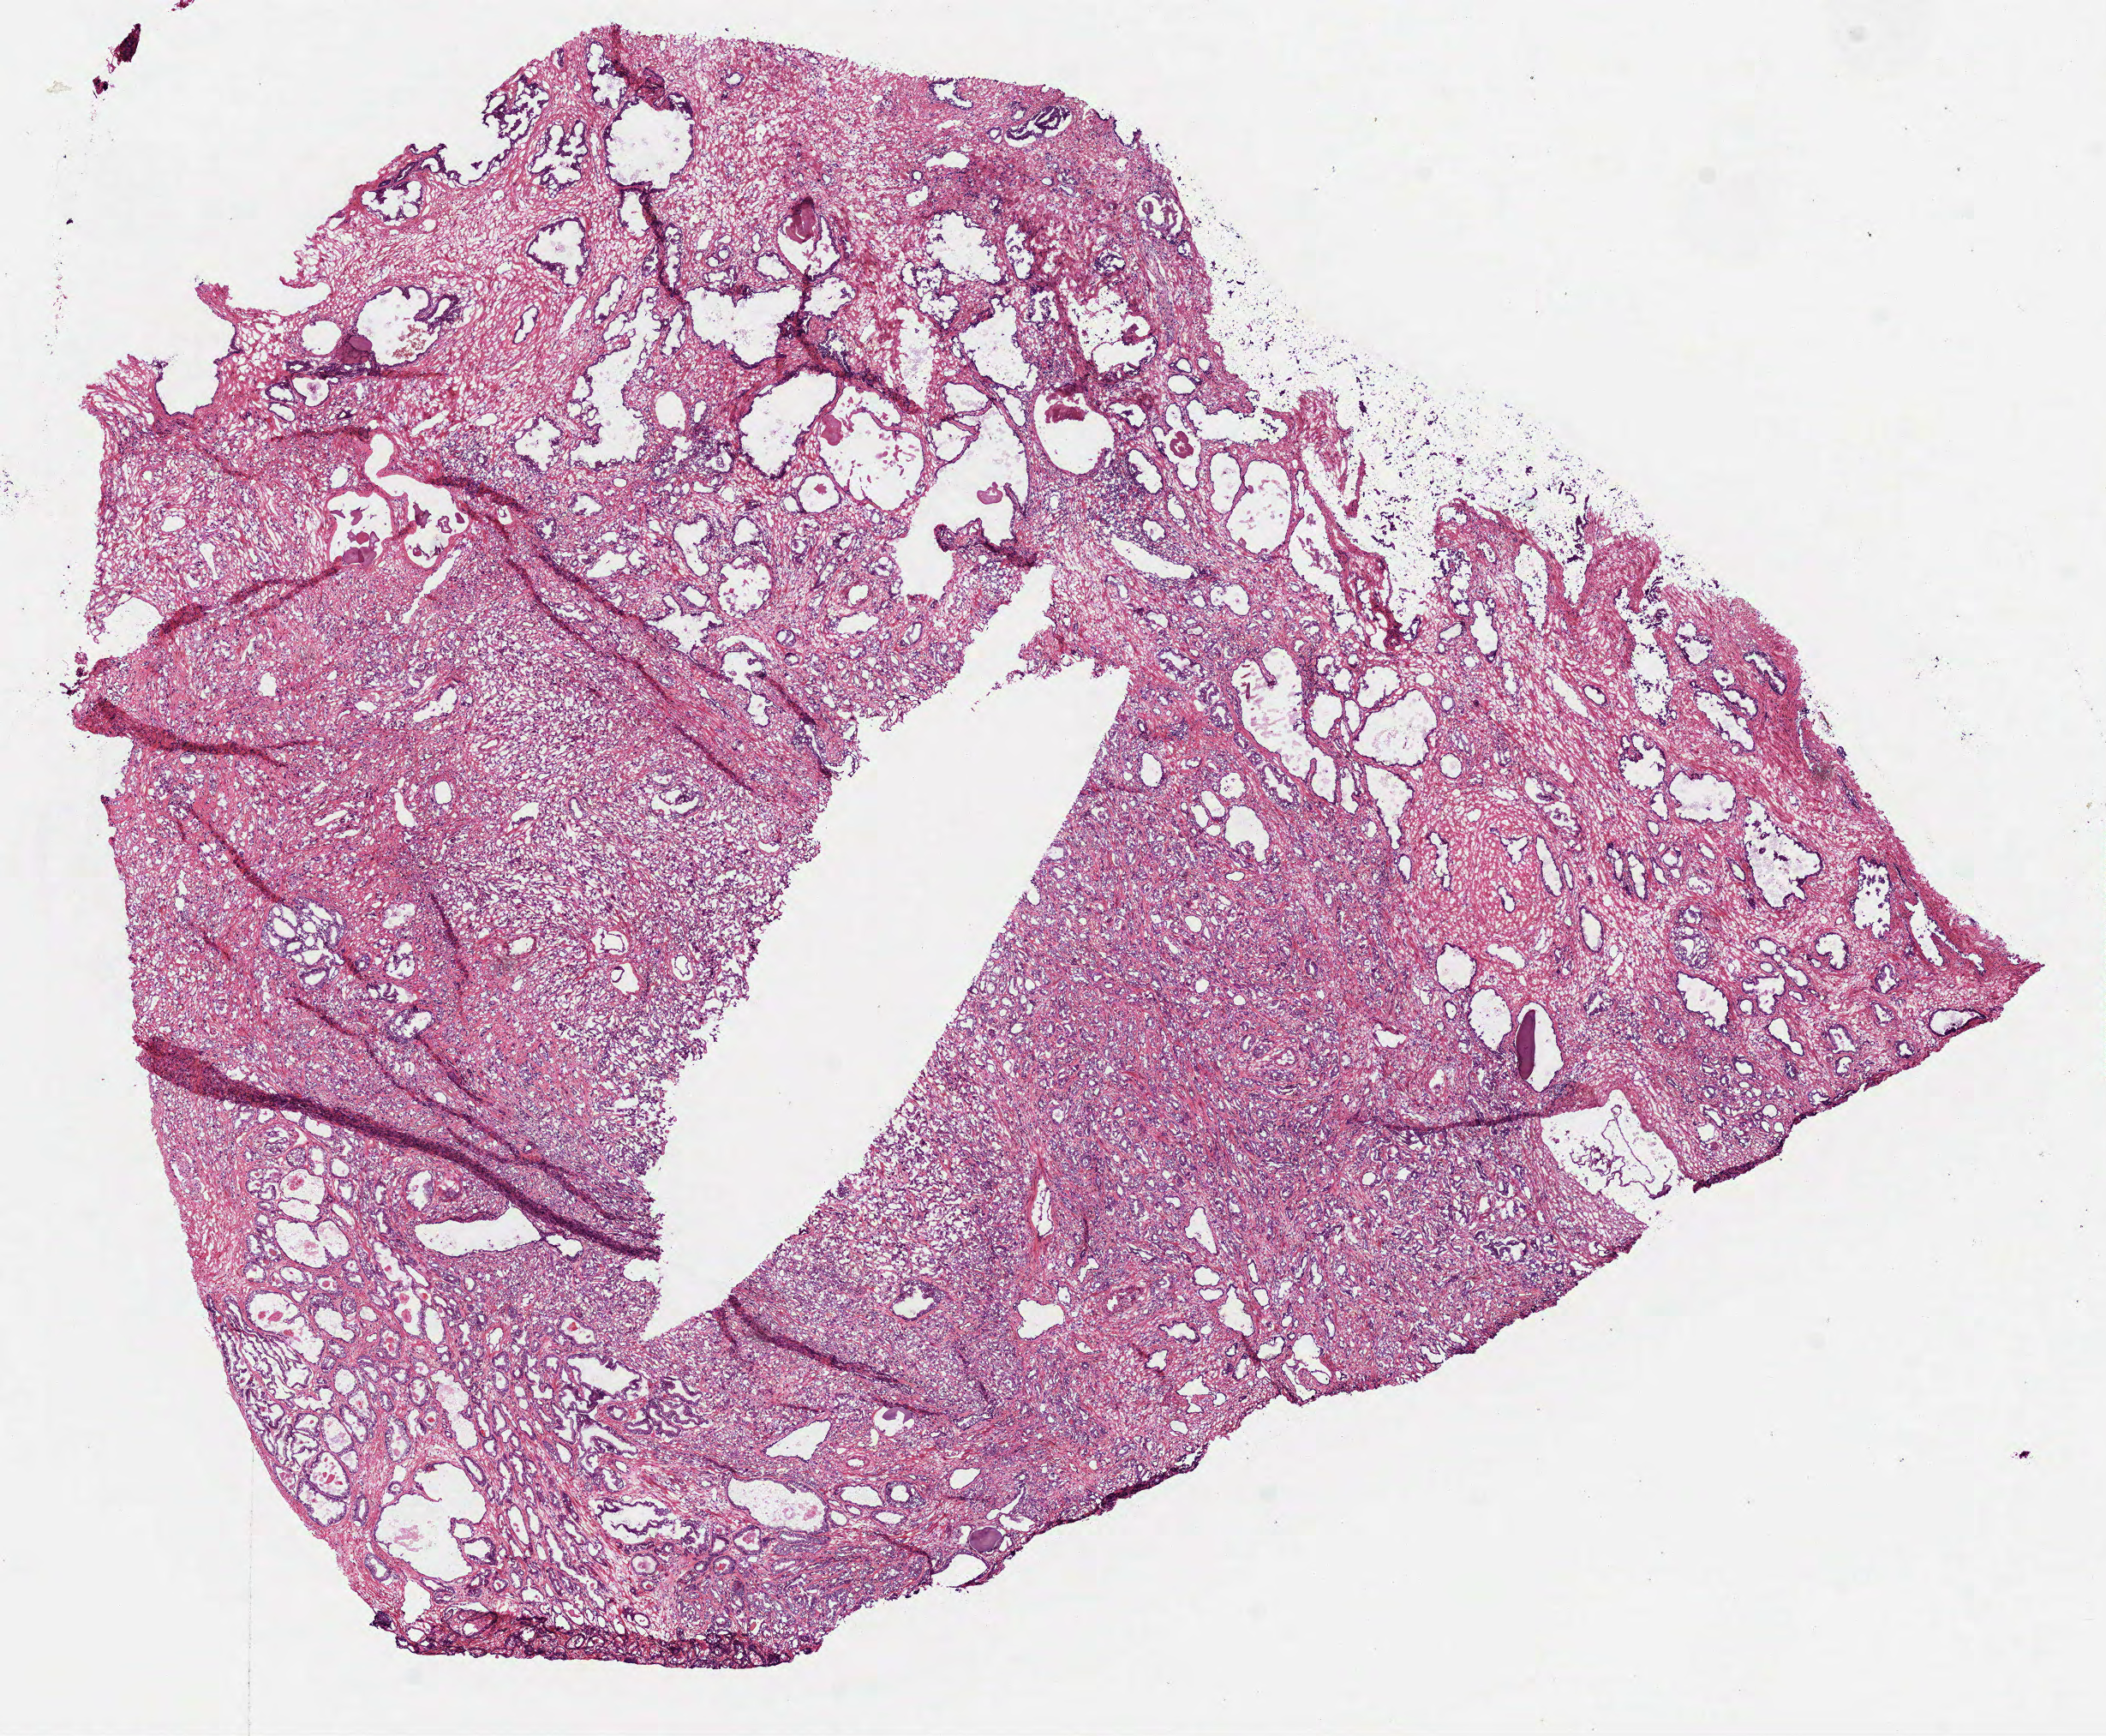
Digitized Hematoxylin and eosin (H&E) stained tissue section (whole slide) — shown as a low-resolution overview of the whole scanned area (about 9.9 x 8.2 mm, from a 40x scan). Frozen section. Prostate, primary tumour sample. Male patient; age at initial diagnosis 66 years. Gleason score: 8 (4+4). Slide review estimates, as recorded: tumour cells 55%, tumour nuclei 55%, normal cells 25%, stromal cells 20%, necrosis 0%.
Lymph nodes positive (case pathology): 0 of 10 examined. Diagnosis: Acinar cell carcinoma (prostate gland).